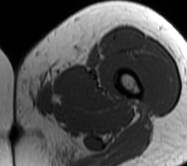
MRI of an extremity soft-tissue mass, one axial slice; position 8 of 62 along the scan axis; MR volume resampled by the dataset authors to the PET/CT grid (not the native acquisition matrix); 3.27 mm slice thickness; 187 × 166 image matrix, field of view 183 × 162 mm. Female patient. From the clinical record (not read from this slice): histological type: leiomyosarcoma; grade: high; site of the primary tumour: groin.
Outlined on this slice (expert contour drawn on MRI and transferred to this co-registered scan by the dataset authors):
- gross tumour volume including surrounding oedema: box from (x=13, y=76) to (x=53, y=116) px